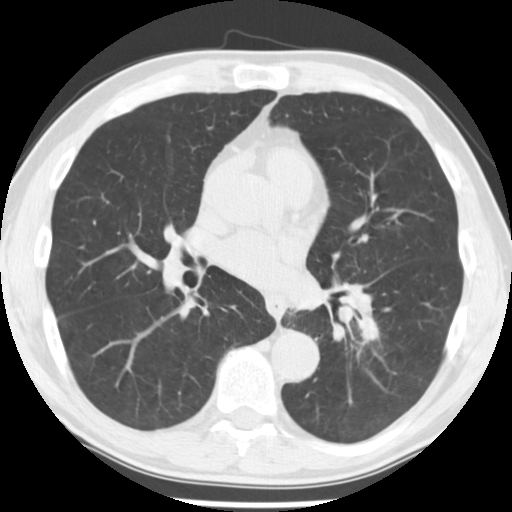
Axial slice from a low-dose chest CT screening exam; third annual screen; lung window (W 1500 / L -600 HU); standard (soft-tissue) reconstruction kernel (STANDARD); 120 kVp; slice 118 of 242 in the series. Male participant, aged 64 years at enrolment.
• Expert reader's lesion annotation, bounding box <350,316,389,351> (left, top, right, bottom; pixels).
• No non-calcified nodule or mass ≥4 mm was recorded by the screening reader at this exam.
• Official screen result: negative screen, no significant abnormalities.
• Participant outcome: lung cancer diagnosed 203 days after this screen — adenocarcinoma, NOS, left lower lobe, stage IV (AJCC 6th edition), 44 mm at pathology.